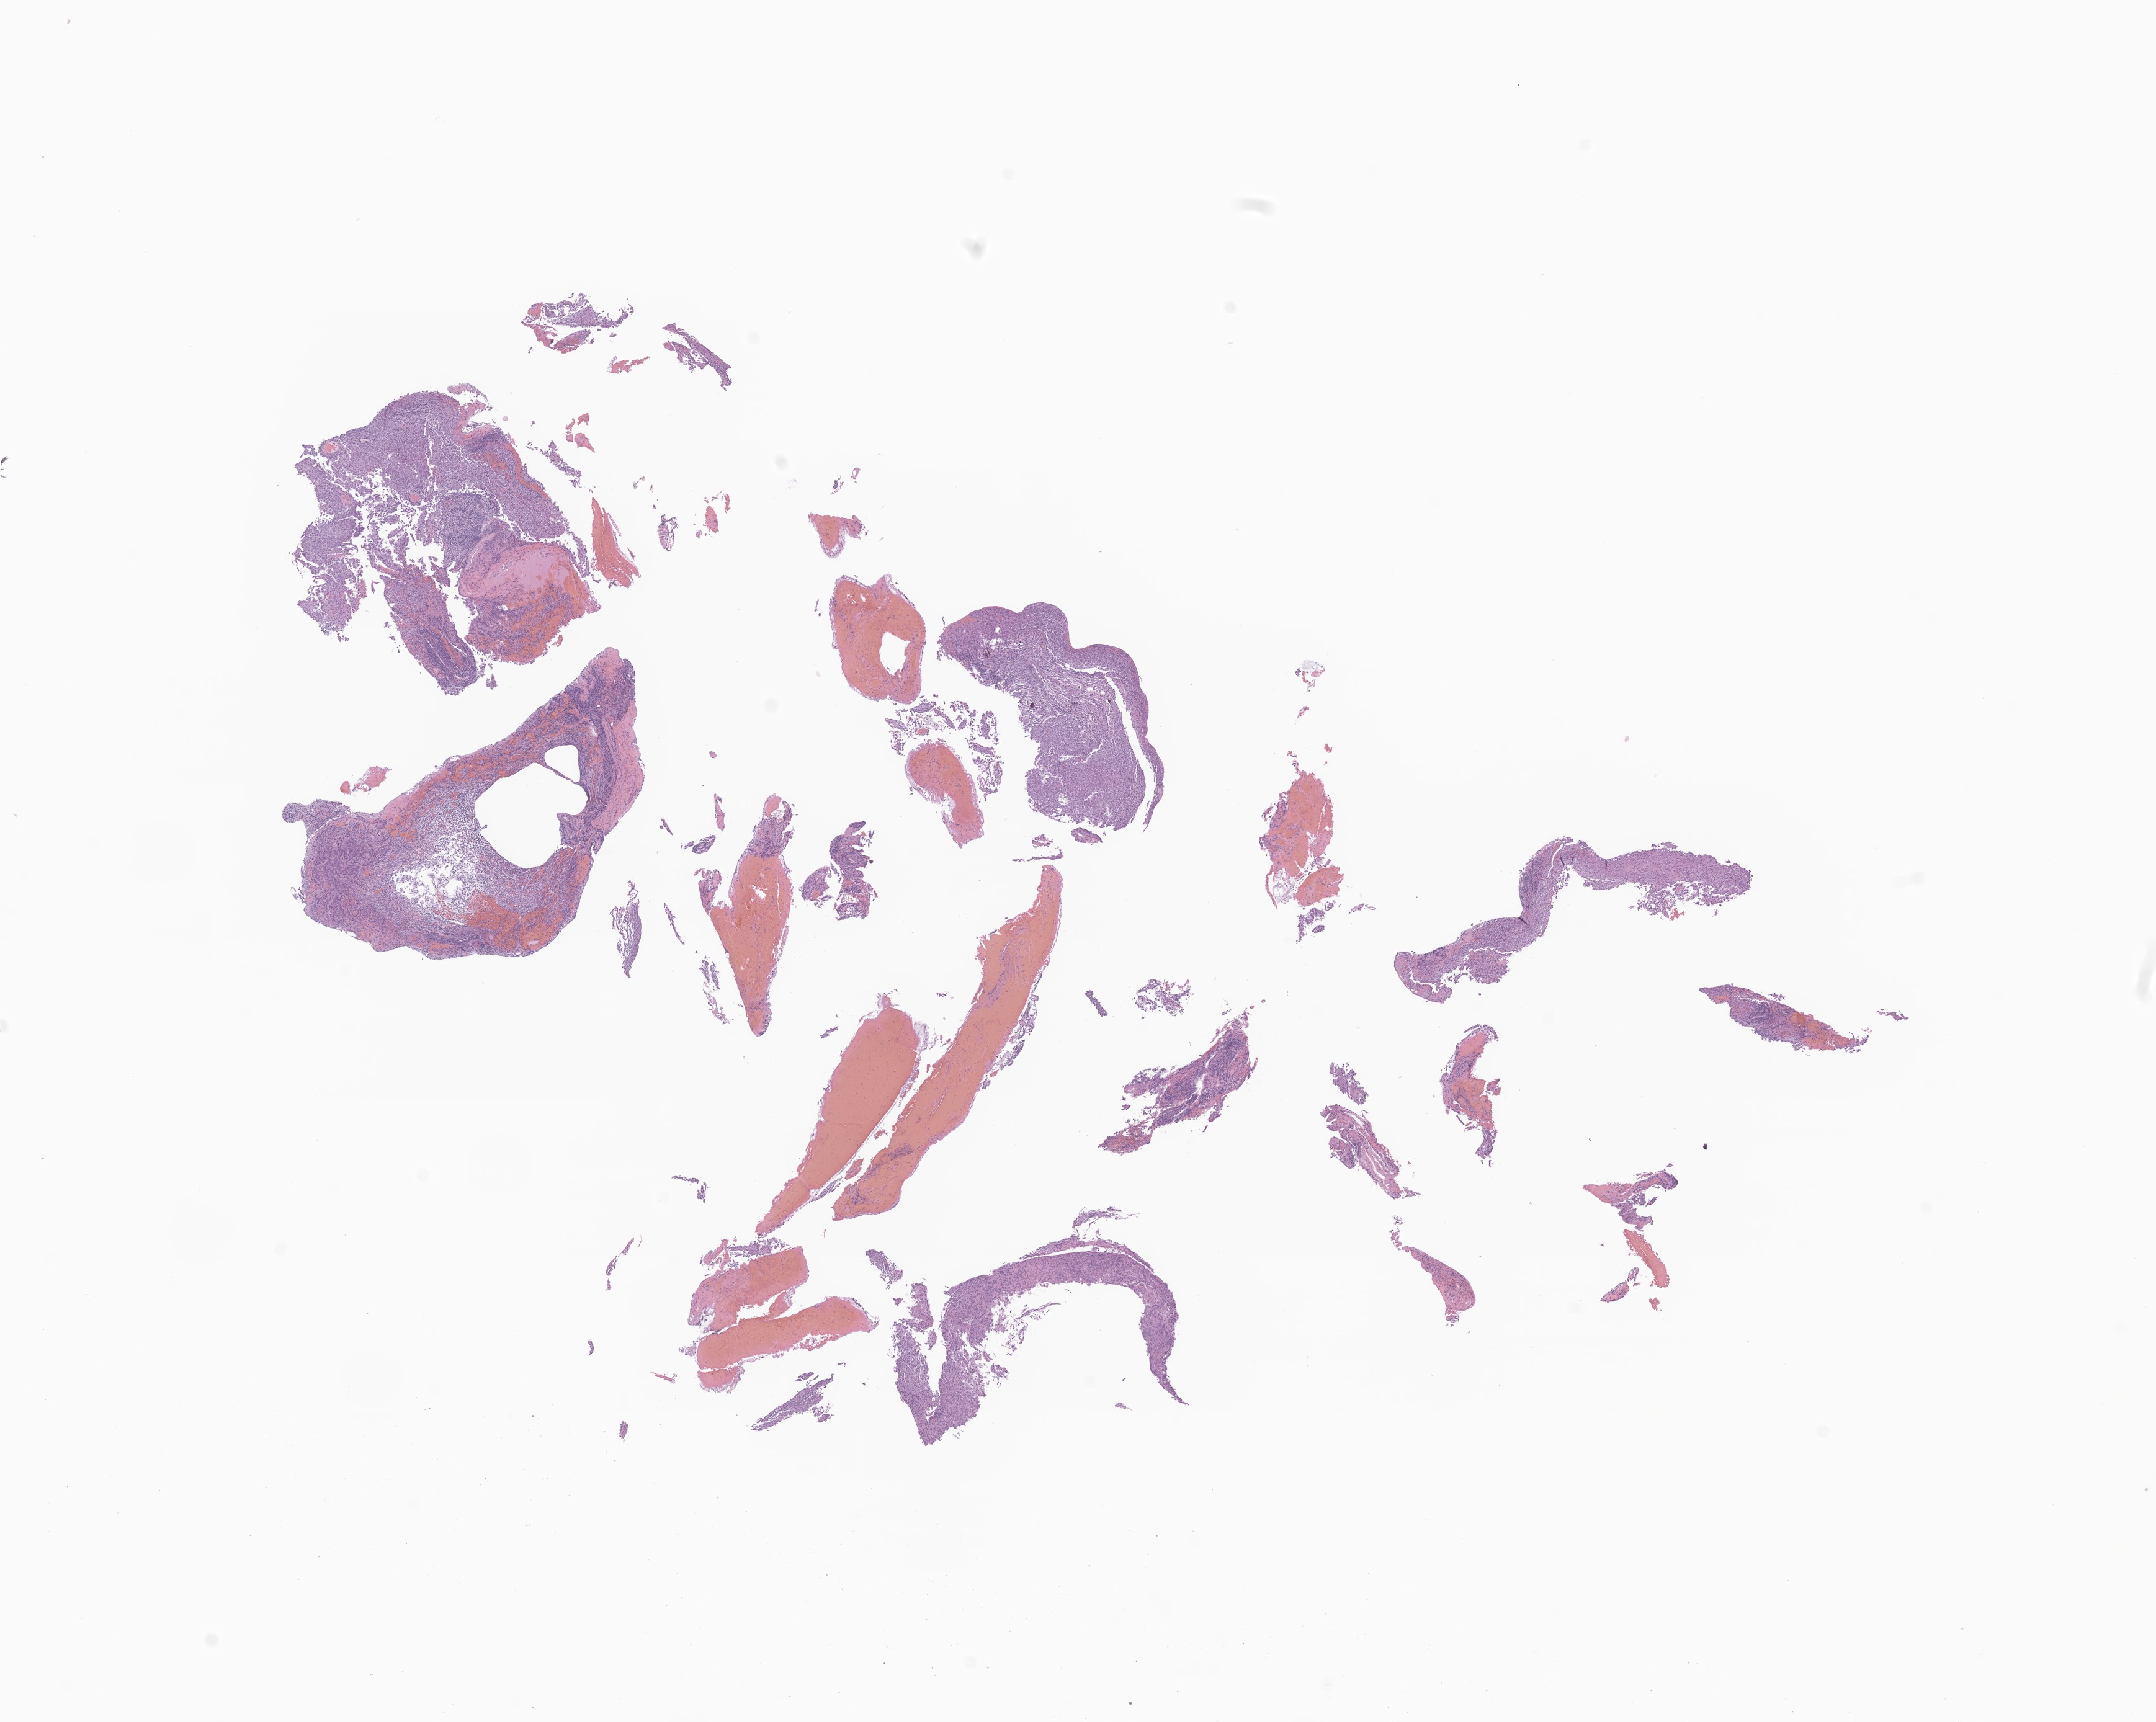
Whole-slide image, H&E stain of tumor tissue from the pineal gland — whole scanned area (about 14.7 x 11.7 mm) shown as a low-resolution overview; FFPE section. Patient: male, age 97 months (8 years 1 month).
• diagnosis: Dysgerminoma